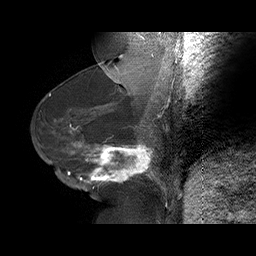
Breast MRI (dynamic contrast-enhanced), one sagittal slice; position 31 of 75 along the scan axis; dynamic contrast-enhanced series, time point 2 of 6 at this slice position (early post-contrast); 1.5 T; TE 4.5 ms, TR 32.4 ms; 3 mm slice thickness; 256 × 256 image matrix, field of view 180 × 180 mm. Female patient. From the clinical record (not read from this slice): setting: breast cancer imaged before/during neoadjuvant chemotherapy; receptor status: HR-positive, HER2-negative.
Annotated regions visible in this slice (semi-automatically segmented with operator editing):
- analysis volume of interest (the breast-tissue region the enhancement analysis was run in; not a lesion): bounding box (x1, y1, x2, y2) in pixels: (58, 134, 166, 191)
- tumour enhancement mask (voxels above the 100 % enhancement threshold inside the analysis volume of interest): (58, 141, 166, 190)